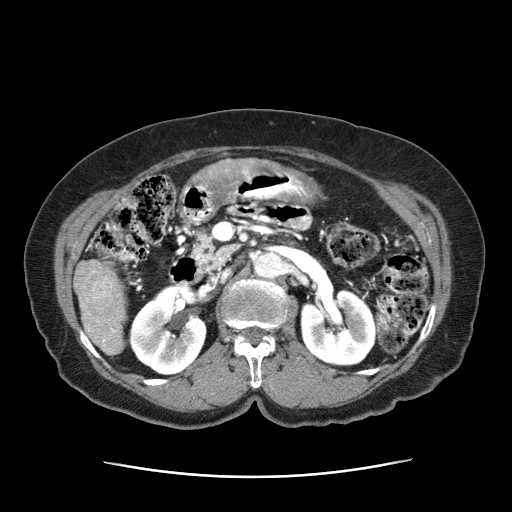
Contrast-enhanced abdominal CT (liver protocol), one axial slice; slice 15 of 63 in the series (ordered by position); reconstruction kernel STANDARD; soft-tissue window (W 400 / L 40 HU); 2.5 mm slice thickness; 512 × 512 image matrix, field of view 360 × 360 mm. Female patient, age 79 years. Case-level facts recorded for this patient, not image findings: diagnosis: hepatocellular carcinoma (patient treated with transarterial chemoembolisation; whether this scan precedes or follows treatment is not stated here); TNM stage (as recorded): Stage-II; Child-Pugh class: B; tumour differentiation: well differentiated; tumour nodularity: multinodular.
Outlined on this slice (semi-automatically segmented with operator editing):
- abdominal aorta: bounding box (x1, y1, x2, y2) in pixels: (254, 250, 284, 278)
- liver parenchyma outside the tumour (the mass and vessels are separate outlines, so this box may not span the whole liver): (73, 259, 129, 356)
- mass: (192, 160, 255, 179)
- liver vessels: (83, 271, 107, 343)